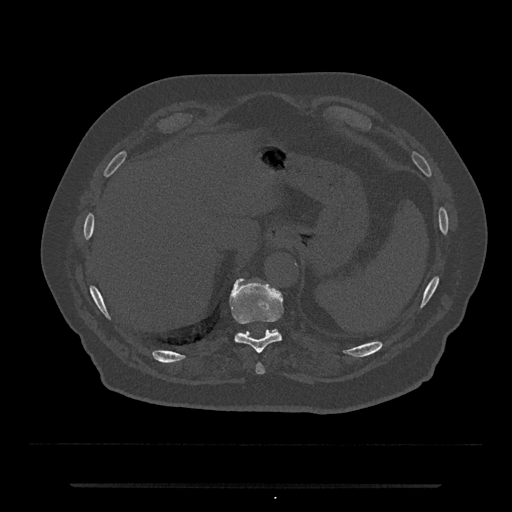
CT including the spine, one axial slice. Position 698 of 797 along the scan axis. Bone window (W 1800 / L 400 HU). 0.5 mm slice thickness. 512 × 512 image matrix. Male patient, age 80 years. Case-level facts recorded for this patient, not image findings: primary cancer: prostate; vertebrae with lytic lesions (as recorded): L1, T11.
Structures marked on this image (semi-automatic segmentation, software-assisted and operator-edited):
- T10 vertebra: bounding box (x1, y1, x2, y2) in pixels: (229, 278, 283, 353)
- T11 vertebra: (271, 329, 278, 333)
- T9 vertebra: (256, 363, 265, 374)